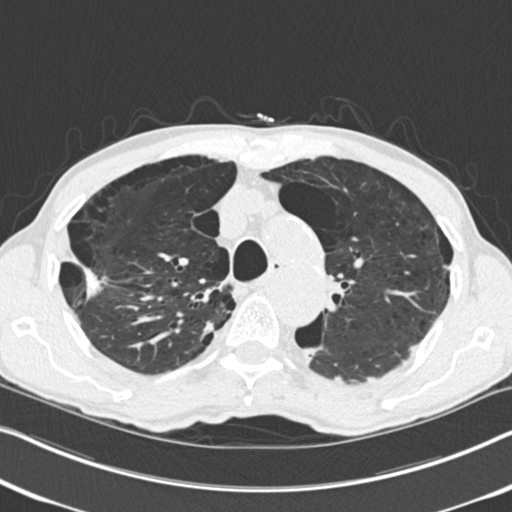
Low-dose screening chest CT, axial slice. Second annual screen. Lung window (W 1500 / L -600 HU). Standard (soft-tissue) reconstruction kernel (B30f). Male, age 71 years at enrolment.
Lesion marked by an expert reader, bounding box <54,238,124,316> (left, top, right, bottom; pixels). The screening reader recorded 4 non-calcified nodules or masses ≥4 mm on this exam (right upper lobe, right upper lobe, right upper lobe, left upper lobe); which of them this box marks is not recorded. Official screen result: positive, change unspecified: nodule(s) >= 4 mm or enlarging nodule(s), mass(es), or other non-specific abnormalities suspicious for lung cancer.